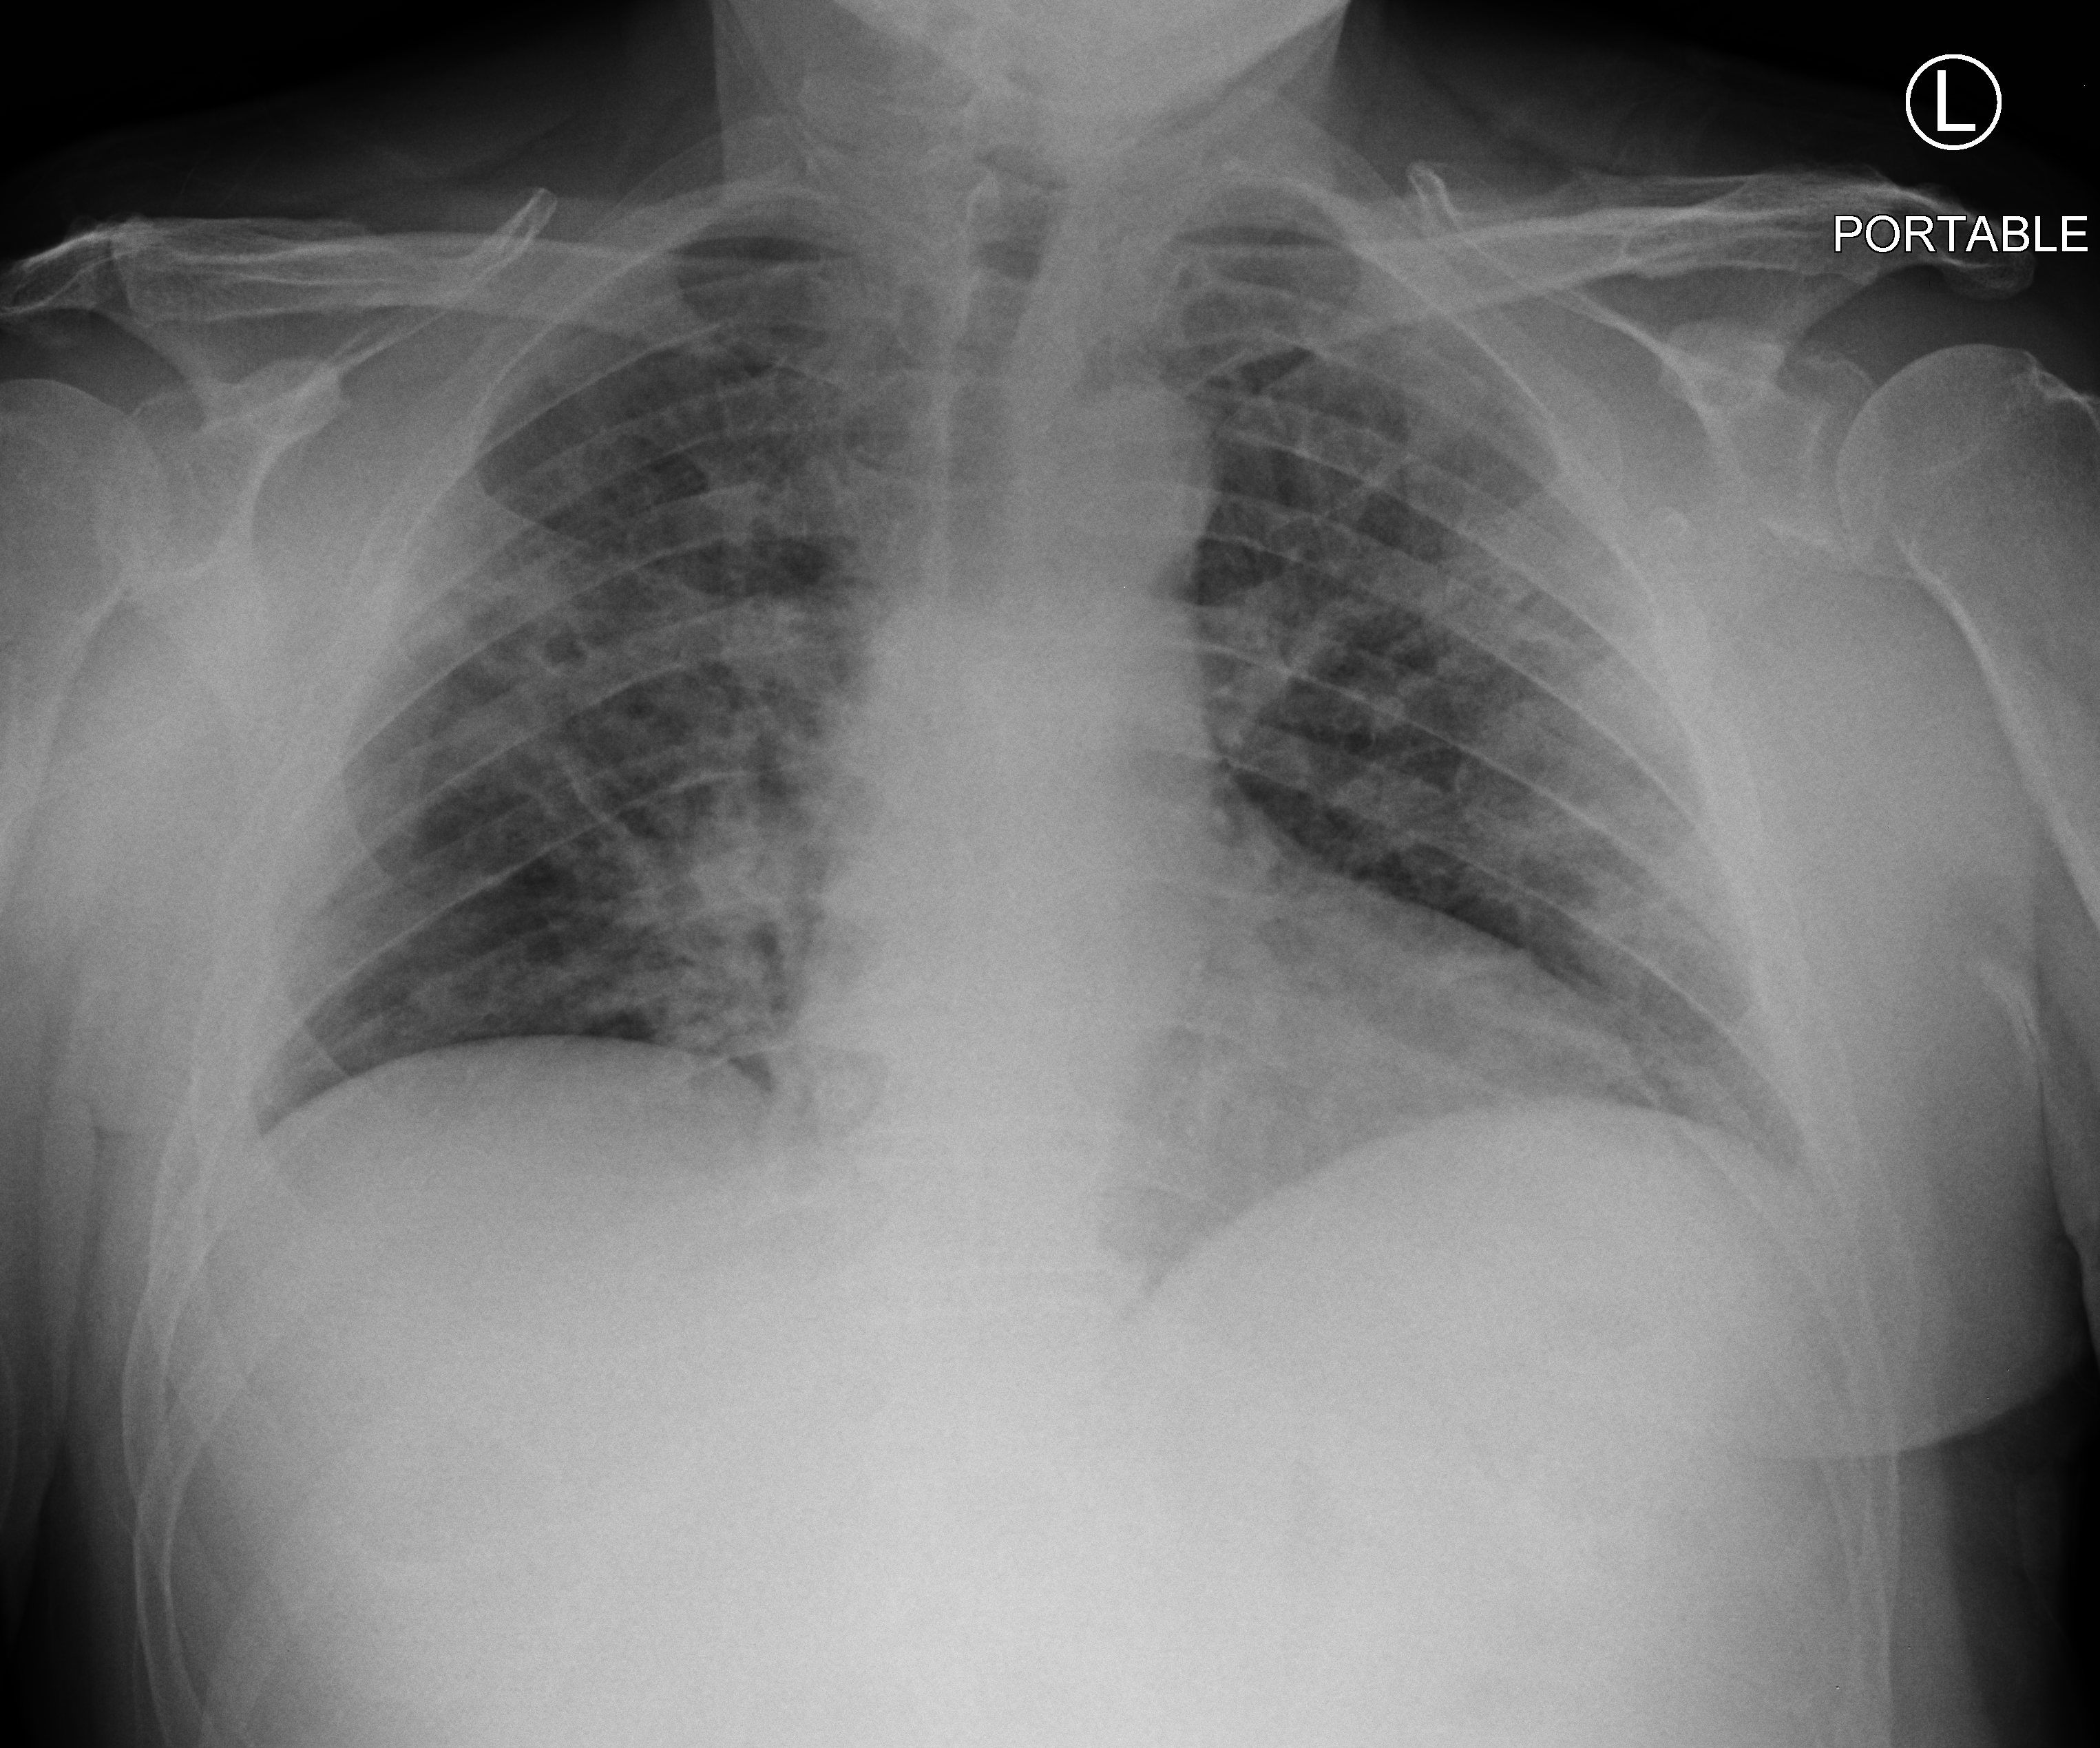
Portable chest radiograph; anteroposterior (AP) projection. Patient hospitalised with COVID-19; male, aged 60–74 years.
Admission-level facts for this patient (not findings on this image; timing relative to this image not recorded): chronic kidney disease (admission record): no; length of hospital stay: 16 days.